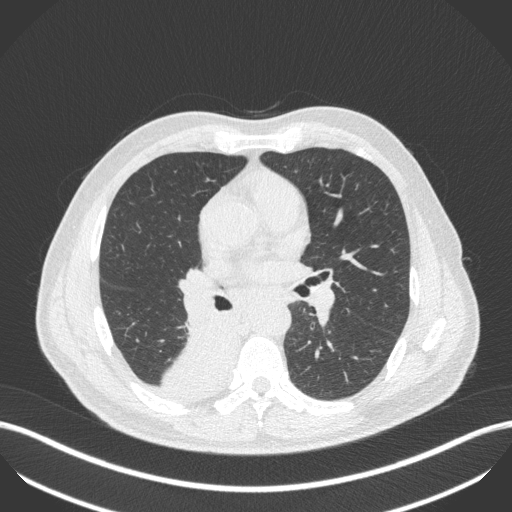
Chest CT, one axial slice. Position 258 of 451 along the scan axis. Reconstruction kernel B31f. 100 kVp. Lung window (W 1500 / L -600 HU). 512 × 512 image matrix, field of view 400 × 400 mm. Patient: male, 61 years. From the clinical record (not read from this slice): clinical TNM (as recorded): T1 N0 M0.
Structures marked on this image (rectangle marked by the reading radiologist):
- lung tumour (recorded histology: small cell carcinoma): bounding box (x1, y1, x2, y2) in pixels: (146, 322, 238, 401)